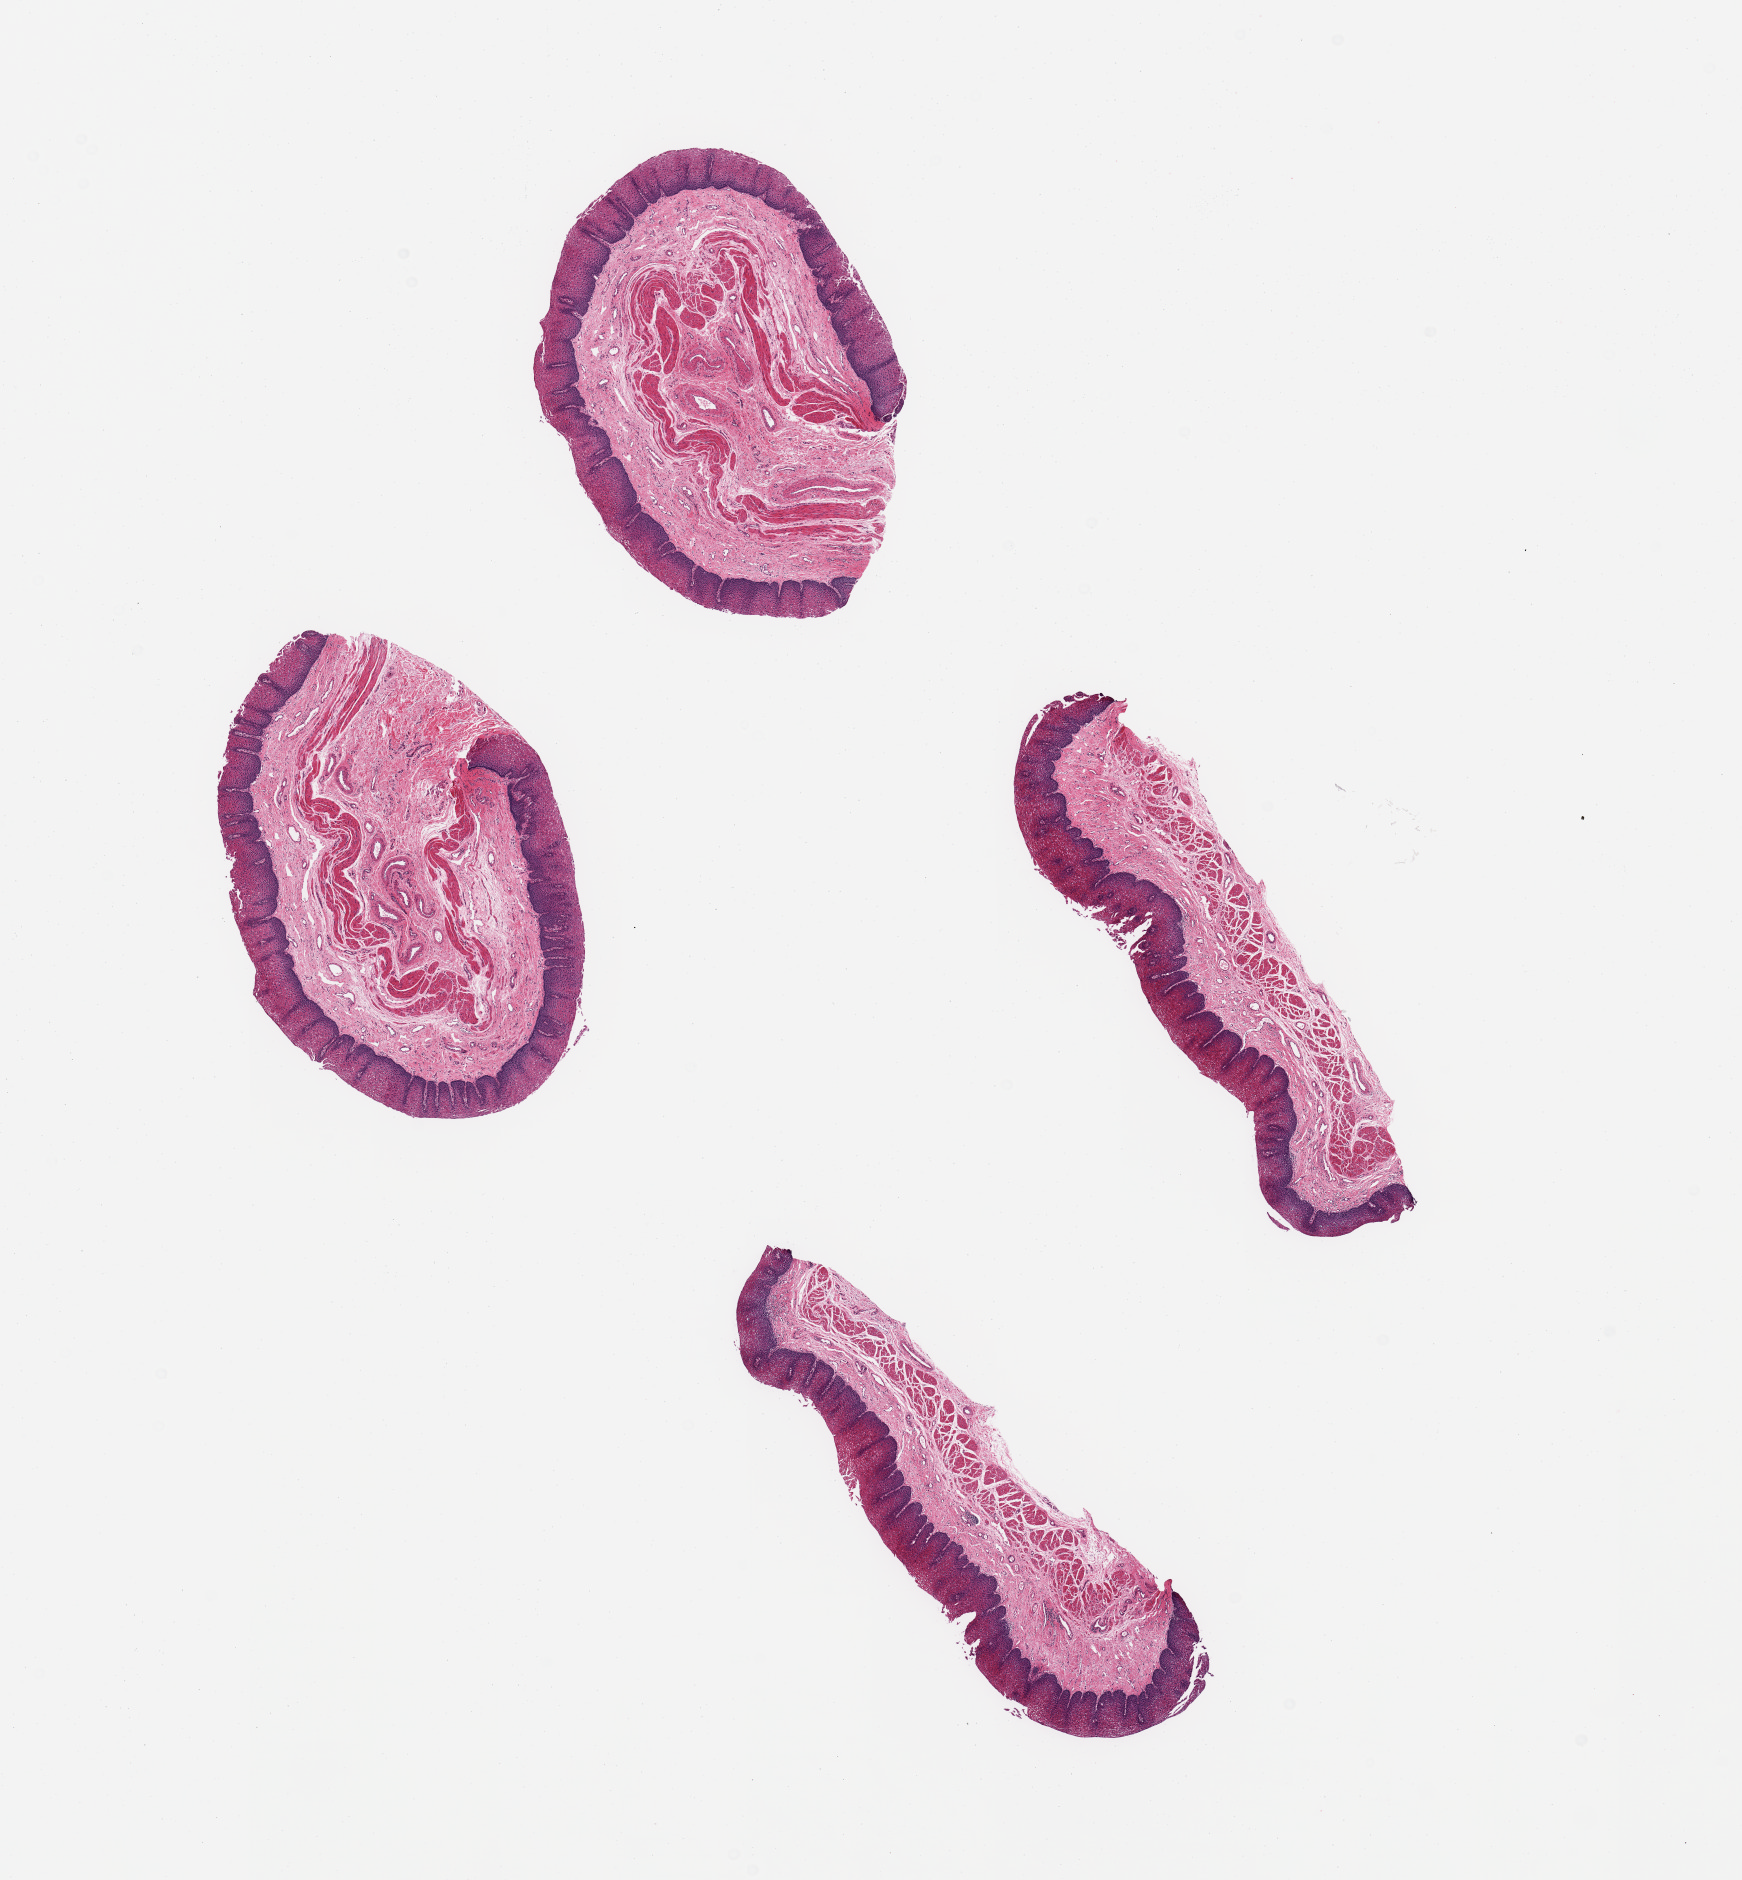
H&E whole-slide image, brightfield, low-resolution overview of the scanned area, about 13.8 x 14.9 mm; PAXgene-fixed, paraffin-embedded tissue; sampled site (target tissue): esophageal mucous membrane; tissue donor sample. Donor: male.
Review note (as recorded): 4 pieces, squamous mucosa up to ~0.4mm, ~30% thickness.